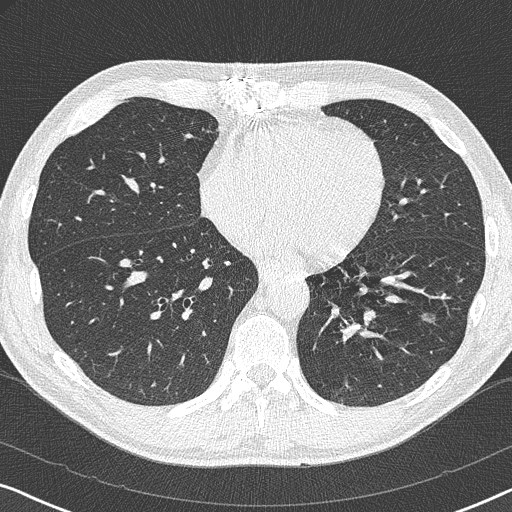
Chest CT (low-dose screening protocol), one axial image. Baseline annual screen. Lung window (W 1500 / L -600 HU). Lung (sharp) reconstruction kernel (B50f). 120 kVp. Slice 214 of 327 in the series. 512 × 512 image matrix. Male participant, aged 59 years at enrolment. Current smoker at enrolment.
• Expert reader's lesion annotation, bounding box [x1, y1, x2, y2] px = [406, 303, 449, 334].
• The screening reader recorded 2 non-calcified nodules or masses ≥4 mm on this exam; which of them this box marks is not recorded.
• Lung cancer was diagnosed 821 days after this screen (after the third annual screen): adenocarcinoma, NOS, left lower lobe, poorly differentiated (G3), stage IA (AJCC 6th edition), 20 mm at pathology.